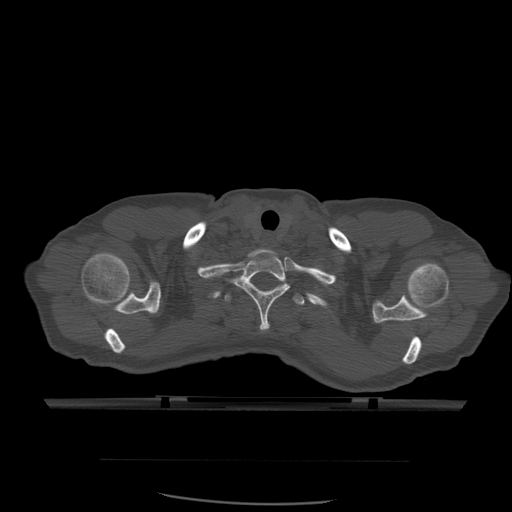
CT including the spine, one axial slice. Position 469 of 574 along the scan axis. Bone window (W 1800 / L 400 HU). 1.25 mm slice thickness. 512 × 512 image matrix, field of view 392 × 392 mm. Patient age 48 years. Case-level facts recorded for this patient, not image findings: primary cancer: lung; vertebrae with lytic lesions (as recorded): T11.
Outlined on this slice (semi-automatically segmented with operator editing):
- T1 vertebra: box from (x=231, y=249) to (x=291, y=332) px
- T2 vertebra: (x=224, y=283)–(x=305, y=306)